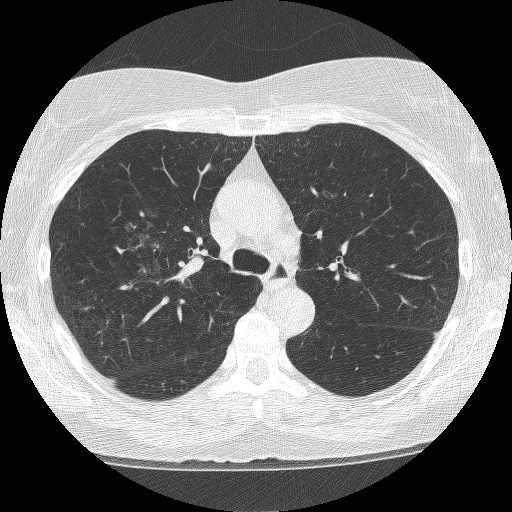
Axial slice from a low-dose chest CT screening exam. Second annual screen. Lung window (W 1500 / L -600 HU). 1.25 mm slice thickness. Lung (sharp) reconstruction kernel (BONE). Slice 167 of 249 in the series. Female, age 64 years at enrolment. Former smoker at enrolment.
• Expert reader's lesion annotation, box from (x=114, y=204) to (x=210, y=294) px.
• The screening reader recorded 4 non-calcified nodules or masses ≥4 mm on this exam (right upper lobe, right upper lobe, right upper lobe, left upper lobe); which of them this box marks is not recorded.
• Official screen result: positive, other.
• Lung cancer was diagnosed 381 days after this screen: adenocarcinoma, NOS, right upper lobe, right middle lobe, right hilum, stage IV (AJCC 6th edition), 85 mm at pathology.